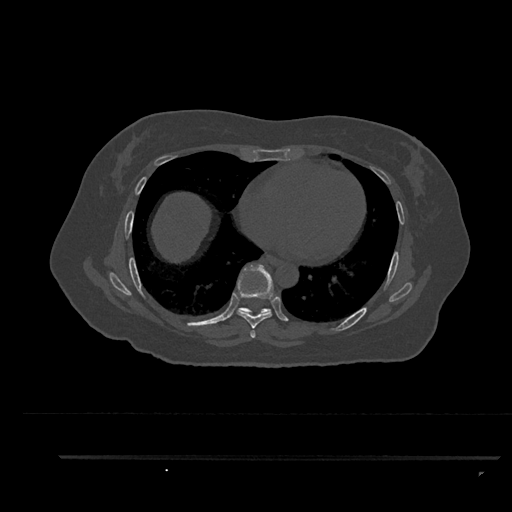
CT including the spine, one axial slice; position 494 of 797 along the scan axis; reconstruction kernel Br40s/3; 120 kVp; bone window (W 1800 / L 400 HU); 0.5 mm slice thickness; 512 × 512 image matrix. Patient: female, 44 years. From the clinical record (not read from this slice): primary cancer: renal; vertebrae with lytic lesions (as recorded): L1.
Annotated regions visible in this slice (semi-automatically segmented with operator editing):
- T6 vertebra: bounding box (x1, y1, x2, y2) in pixels: (251, 334, 255, 338)
- T7 vertebra: (236, 264, 274, 338)
- T8 vertebra: (236, 308, 271, 316)